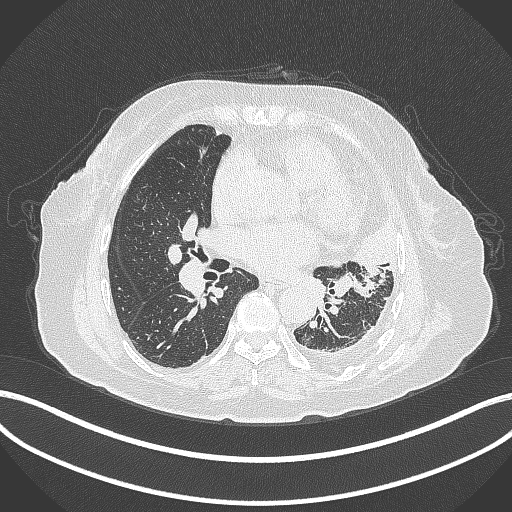
Chest CT, one axial slice. Position 178 of 399 along the scan axis. Reconstruction kernel B70f. Lung window (W 1500 / L -600 HU). 512 × 512 image matrix, field of view 400 × 400 mm. Patient: female, 75 years. From the clinical record (not read from this slice): clinical TNM (as recorded): T3 N3 M1.
Outlined on this slice (rectangle marked by the reading radiologist):
- lung tumour (recorded histology: adenocarcinoma): box from (x=353, y=222) to (x=406, y=272) px